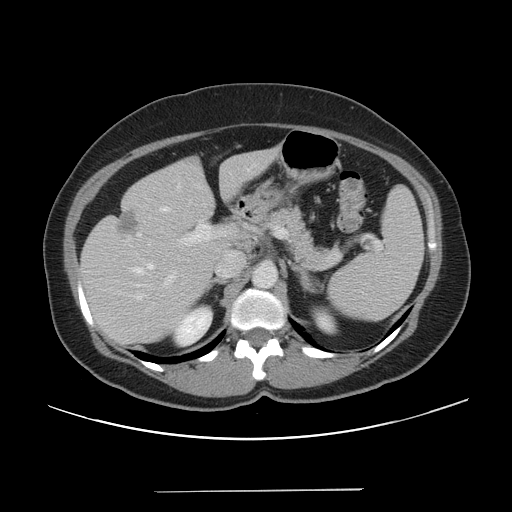
Contrast-enhanced abdominal CT, one axial slice; slice 27 of 56 in the series (ordered by position); 120 kVp; intravenous contrast given; soft-tissue window (W 400 / L 40 HU); 5 mm slice thickness; 512 × 512 image matrix, field of view 419 × 419 mm. Female patient, age 54 years. From the clinical record (not read from this slice): diagnosis: colorectal cancer liver metastases, imaged before liver resection; multiple liver metastases: yes; largest metastasis: 3.2 cm; disease in both lobes: yes.
Outlined on this slice (expert manual segmentation):
- hepatic veins: bounding box (x1, y1, x2, y2) in pixels: (131, 207, 168, 301)
- liver: (81, 147, 280, 346)
- planned liver remnant (the part of the liver to remain after resection): (172, 147, 280, 243)
- portal vein (with intrahepatic branches): (165, 224, 286, 285)
- liver metastasis: (117, 209, 139, 237)